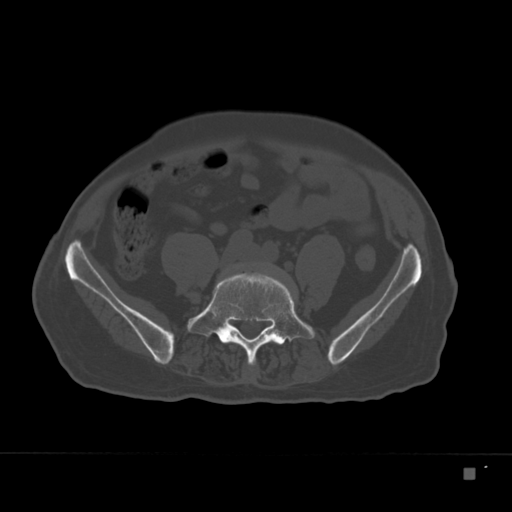
CT including the spine, one axial slice. 120 kVp. Bone window (W 1800 / L 400 HU). 1.5 mm slice thickness. 512 × 512 image matrix, field of view 389 × 389 mm. Male patient, age 72 years. From the clinical record (not read from this slice): primary cancer: skeletal.
Outlined on this slice (semi-automatically segmented with operator editing):
- L5 vertebra: box from (x=192, y=273) to (x=315, y=365) px